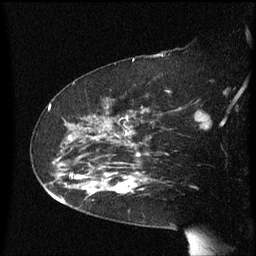
Breast MRI (dynamic contrast-enhanced), one sagittal slice; position 40 of 60 along the scan axis; dynamic contrast-enhanced series, image 2 of 3 at this slice position (ordered by acquisition); 1.5 T; TE 4.2 ms, TR 8.4 ms; 2.3 mm slice thickness; 256 × 256 image matrix. Female patient, age 63 years. Case-level facts recorded for this patient, not image findings: setting: breast cancer imaged before/during neoadjuvant chemotherapy; receptor status: HER2-positive.
Outlined on this slice (semi-automatically segmented with operator editing):
- analysis volume of interest (the breast-tissue region the enhancement analysis was run in; not a lesion): bounding box (x1, y1, x2, y2) in pixels: (71, 144, 147, 207)
- tumour enhancement mask (voxels above the 70 % enhancement threshold inside the analysis volume of interest): (76, 154, 142, 195)